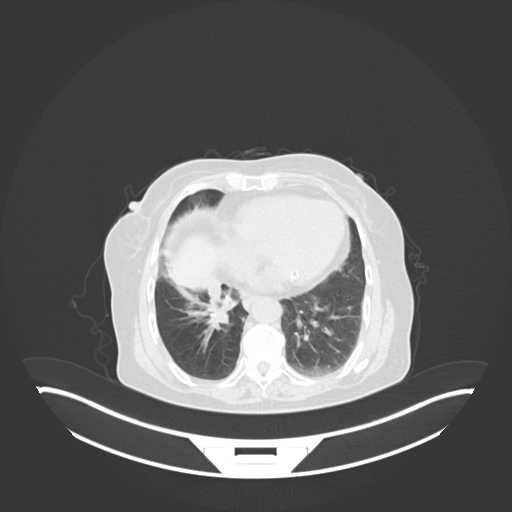
Chest CT, one axial slice. Position 15 of 76 along the scan axis. 120 kVp. Lung window (W 1500 / L -600 HU). 3 mm slice thickness. 512 × 512 image matrix. Female patient, age 75 years. Case-level facts recorded for this patient, not image findings: clinical TNM (as recorded): T1b N0 M1a; histopathological grade: G1.
Structures marked on this image (rectangle marked by the reading radiologist):
- lung tumour (recorded histology: squamous cell carcinoma): bounding box [x1, y1, x2, y2] px = [204, 289, 236, 331]